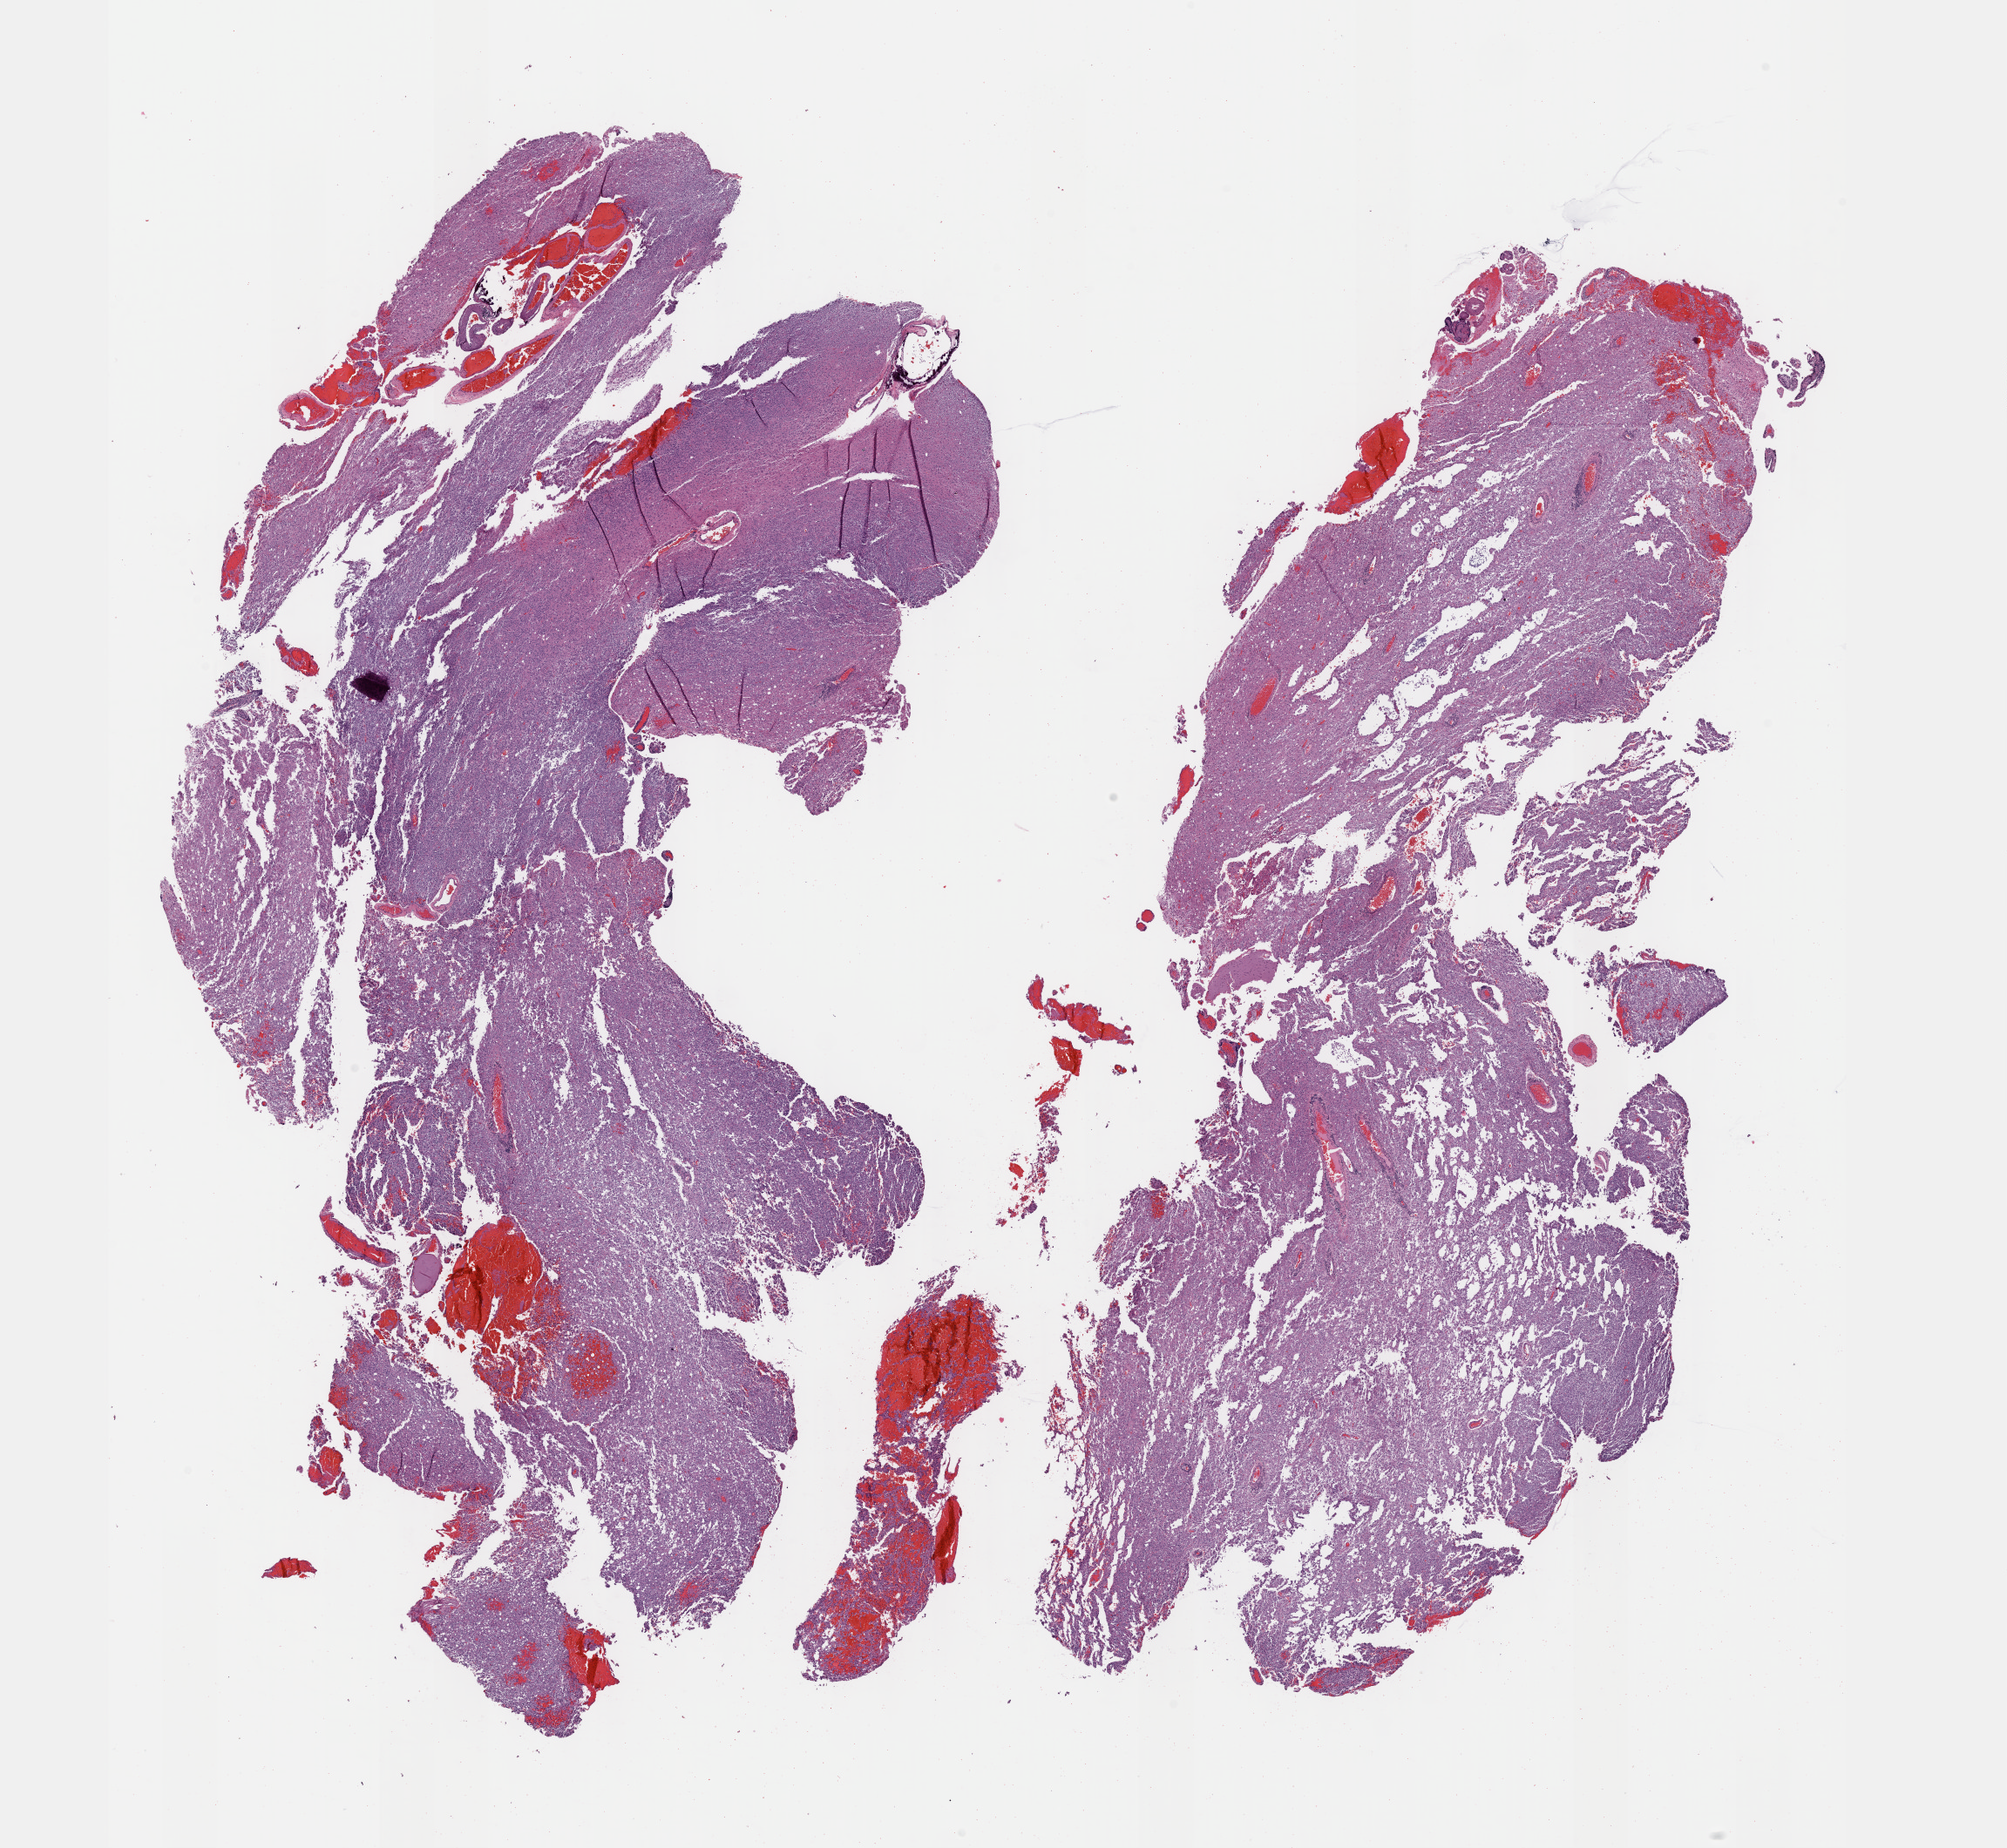
Whole-slide histology image, H&E, shown as a low-resolution overview of the whole scanned area (about 18.6 x 17.1 mm), formalin-fixed paraffin-embedded (FFPE) diagnostic section, primary tumour sample from the brain. Male, age 35 years at initial diagnosis. Histologic grade: G3 (poorly differentiated).
Diagnosis: Oligodendroglioma, anaplastic (cerebrum).